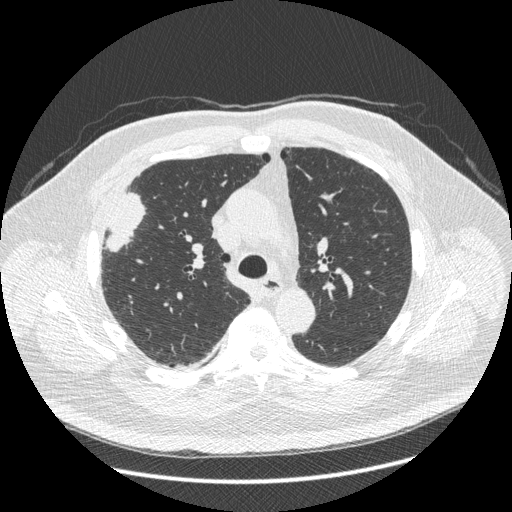
Low-dose screening chest CT, one axial slice; position 291 of 426 along the scan axis; reconstruction kernel STANDARD; lung window (W 1500 / L -600 HU); 1.25 mm slice thickness; 512 × 512 image matrix, field of view 400 × 400 mm.
Outlined on this slice (expert manual segmentation):
- lesion 1 (tumor, upper lobe of right lung): box from (x=106, y=192) to (x=145, y=252) px